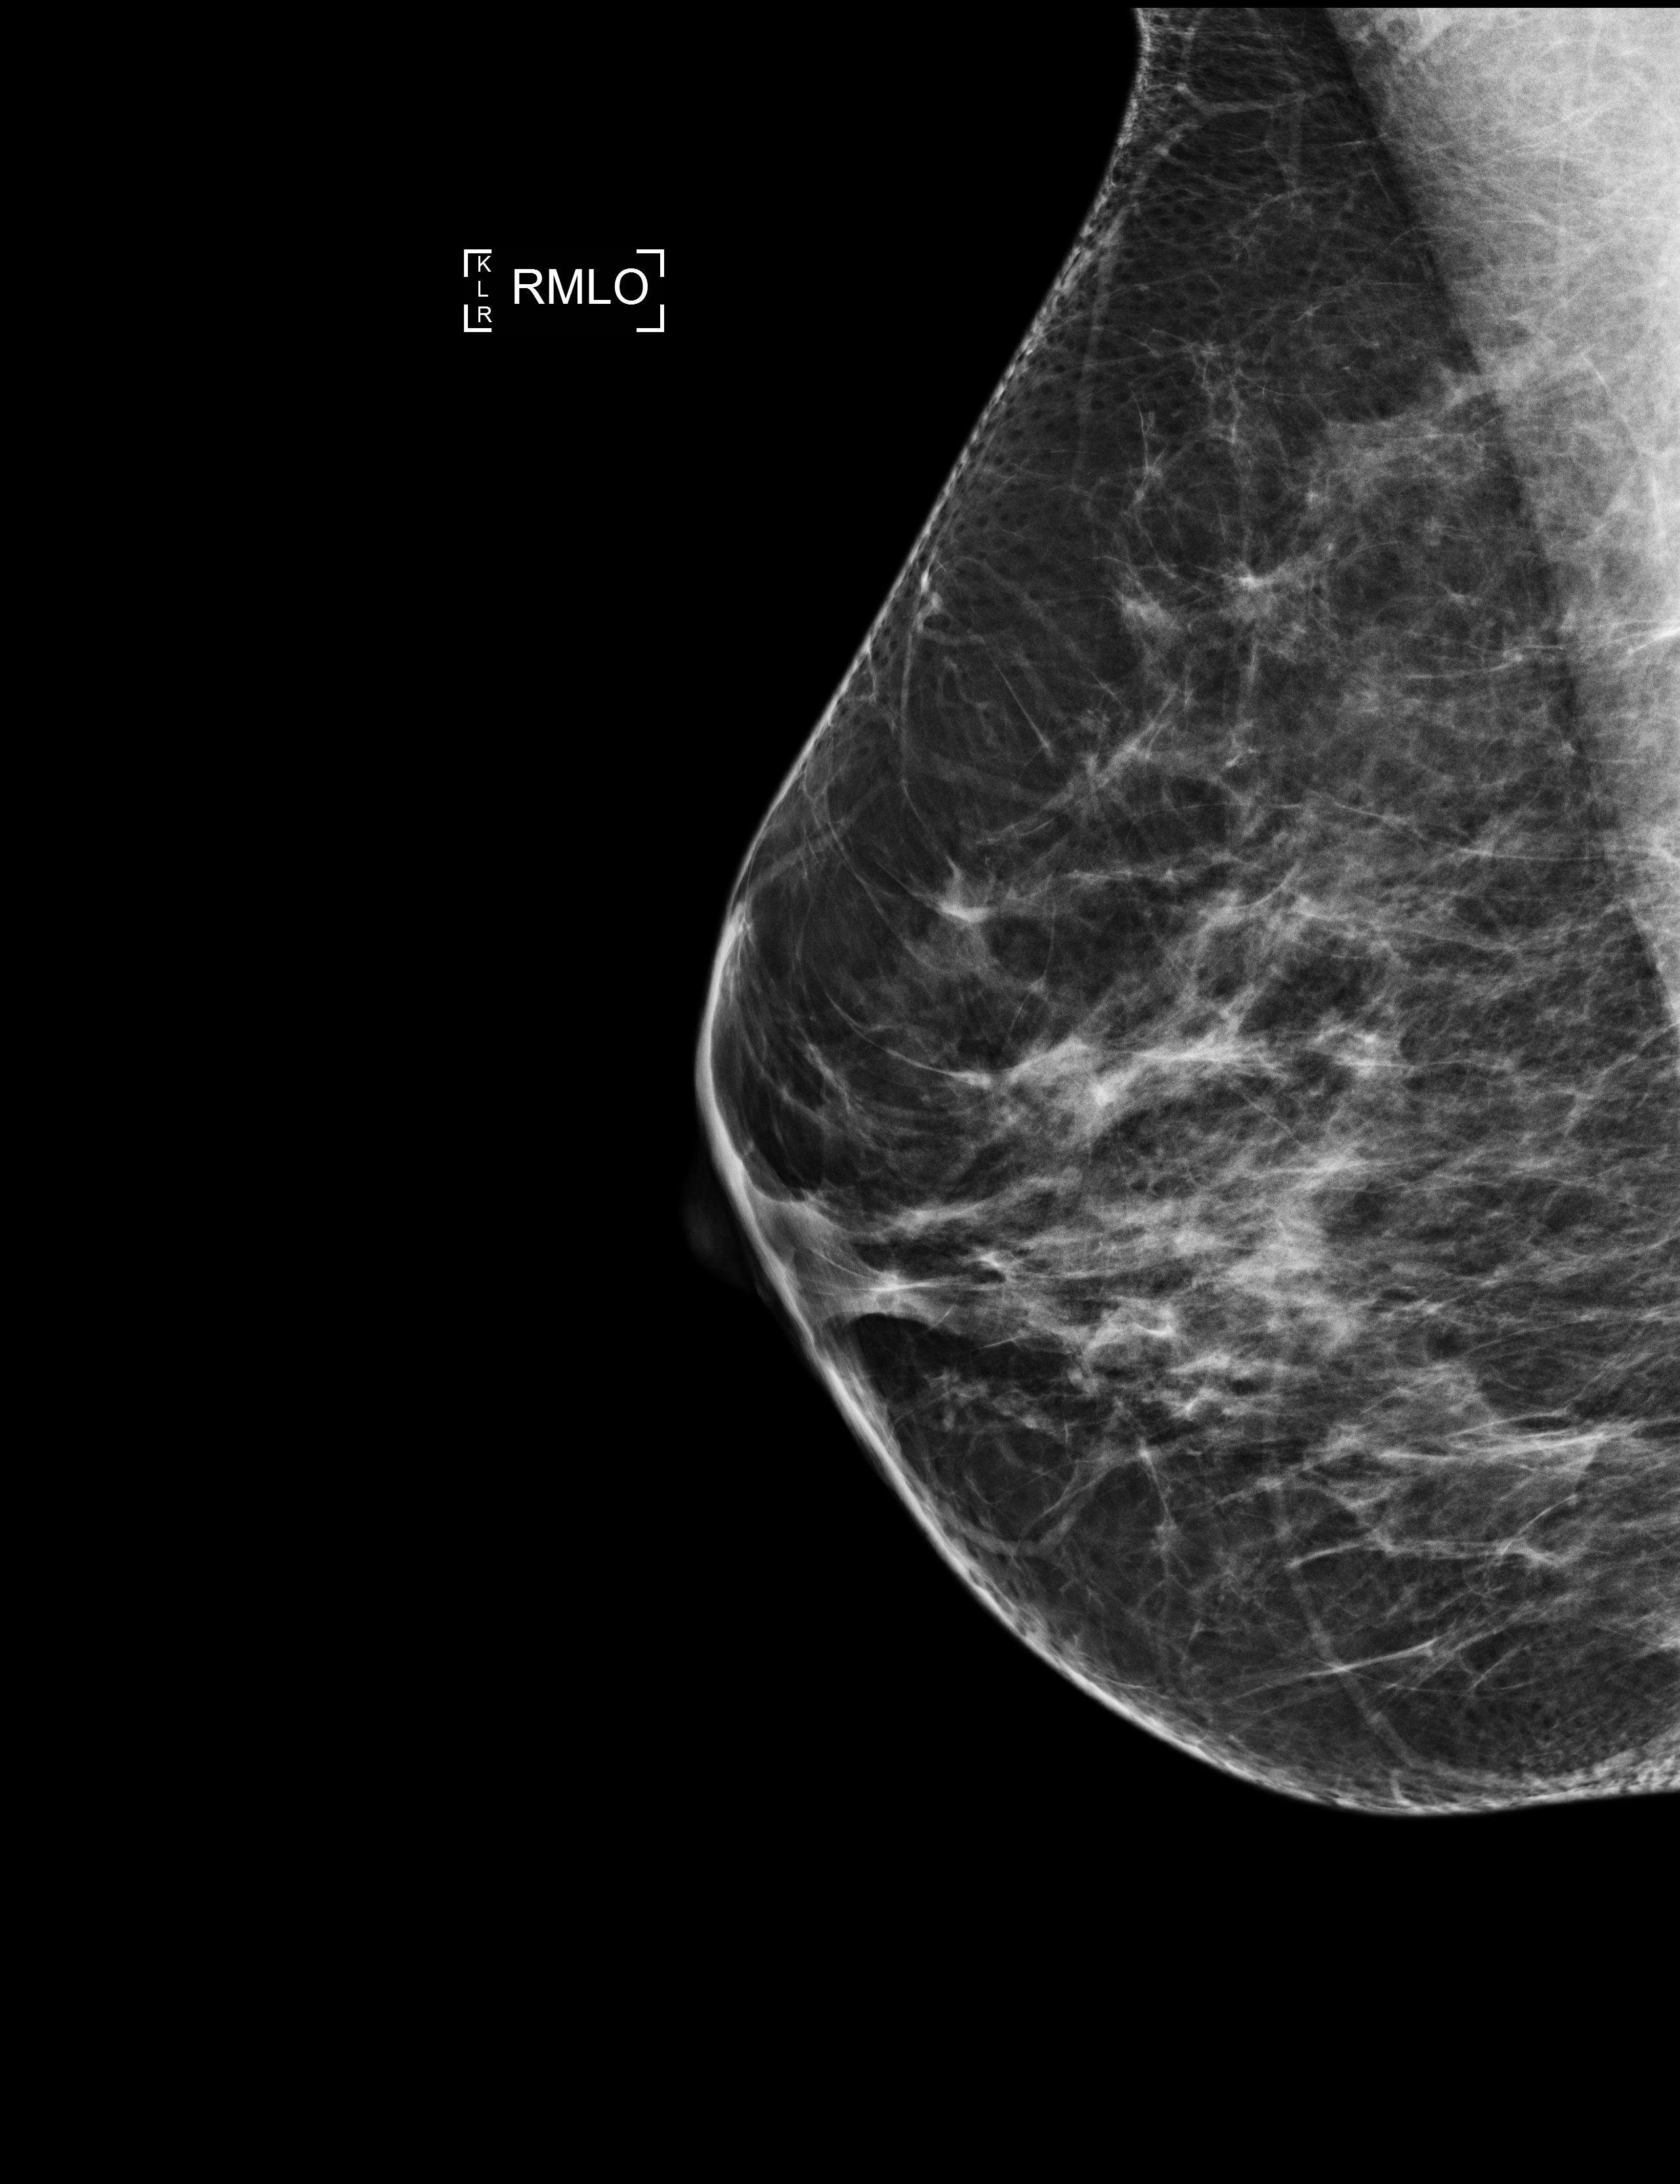
Full-field digital mammogram (FFDM), right breast, medio-lateral oblique projection, annual screening mammography examination, compressed breast thickness 72 mm. Patient: female, 47 years.
- breast density at the screening exam (both breasts): scattered fibroglandular densities (BI-RADS density category b)
- final BI-RADS category for the screening round (tomosynthesis exam, both breasts): category 1
- recall: no recall after this screen